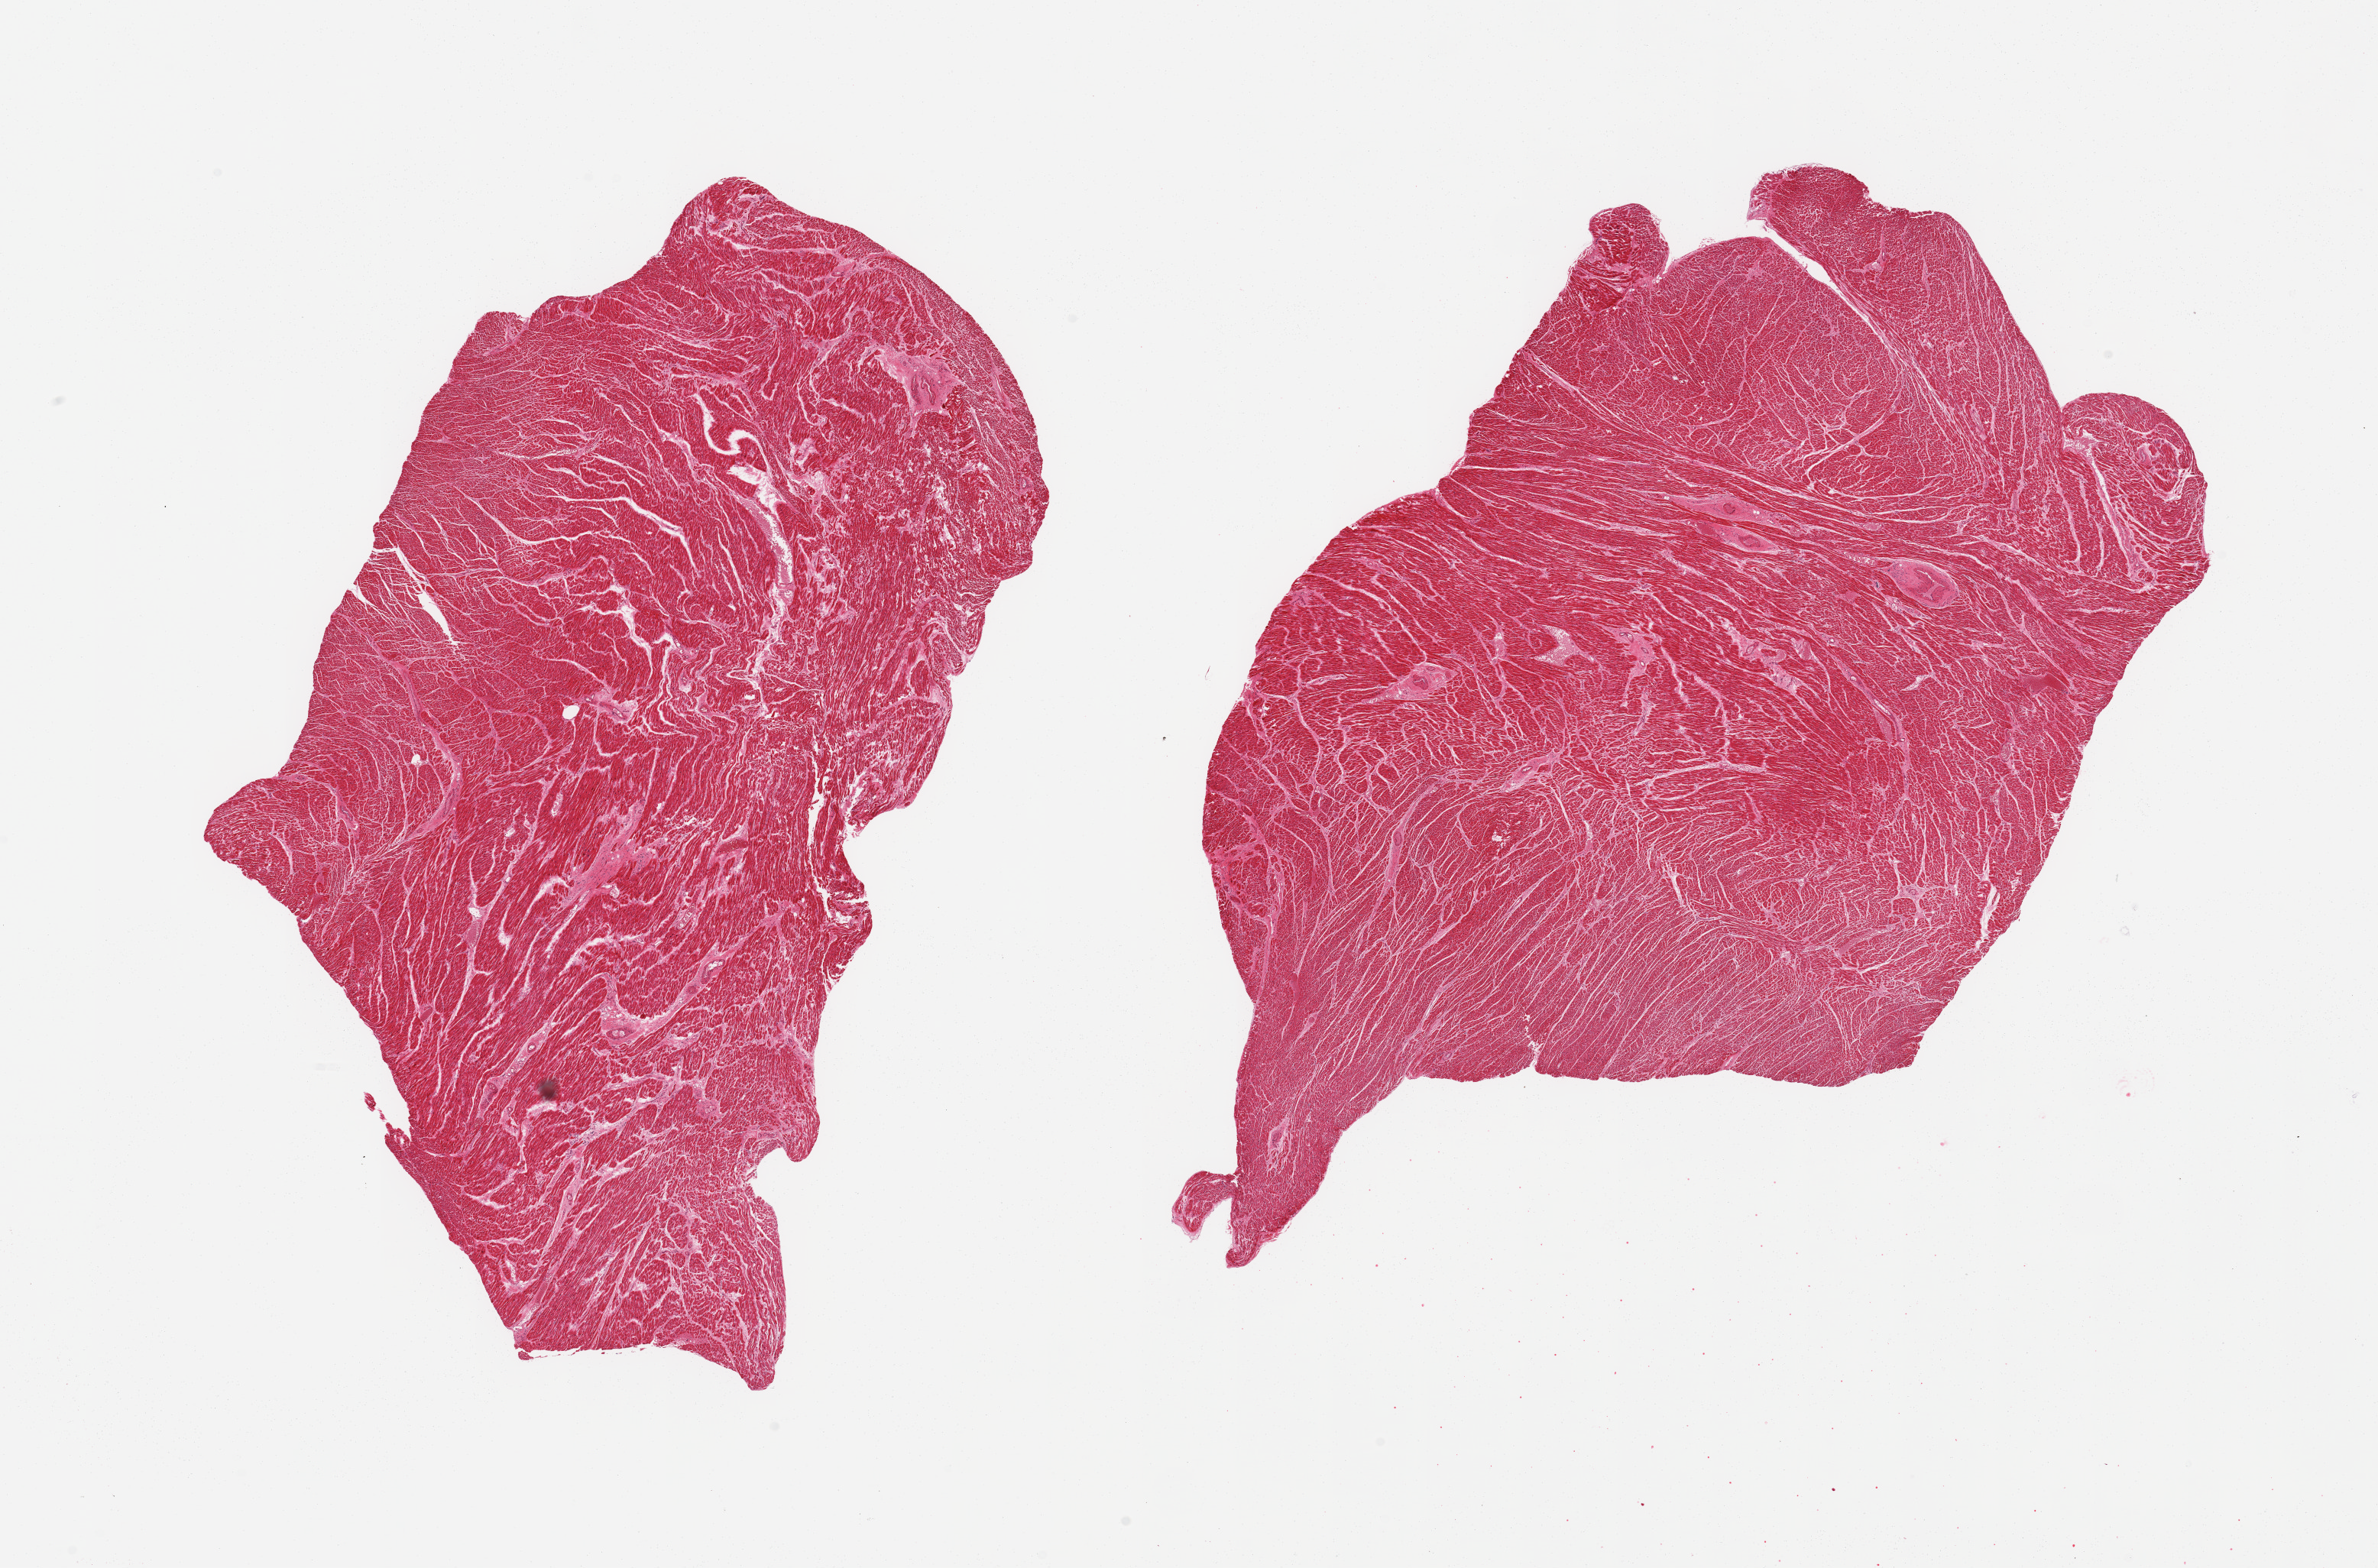
Digitized H&E-stained section, a low-resolution overview of the entire scanned area, about 24.6 x 16.2 mm; PAXgene-fixed paraffin-embedded (PFPE) section; section of heart (target tissue); donor tissue sample. Donor sex: male.
Review note (as recorded): 2 pieces; interstitial fibrosis with scarring.